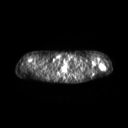
FDG PET of an extremity soft-tissue mass (from a PET/CT study), one axial slice. Position 210 of 267 along the scan axis. 3.27 mm slice thickness. 128 × 128 image matrix, field of view 600 × 600 mm. Patient: female, 28 years. From the clinical record (not read from this slice): histological type: malignant fibrous histiocytoma; grade: low; site of the primary tumour: left arm.
Outlined on this slice (expert contour drawn on MRI and transferred to this co-registered scan by the dataset authors):
- gross tumour volume (mass): bounding box [x1, y1, x2, y2] px = [99, 63, 106, 70]